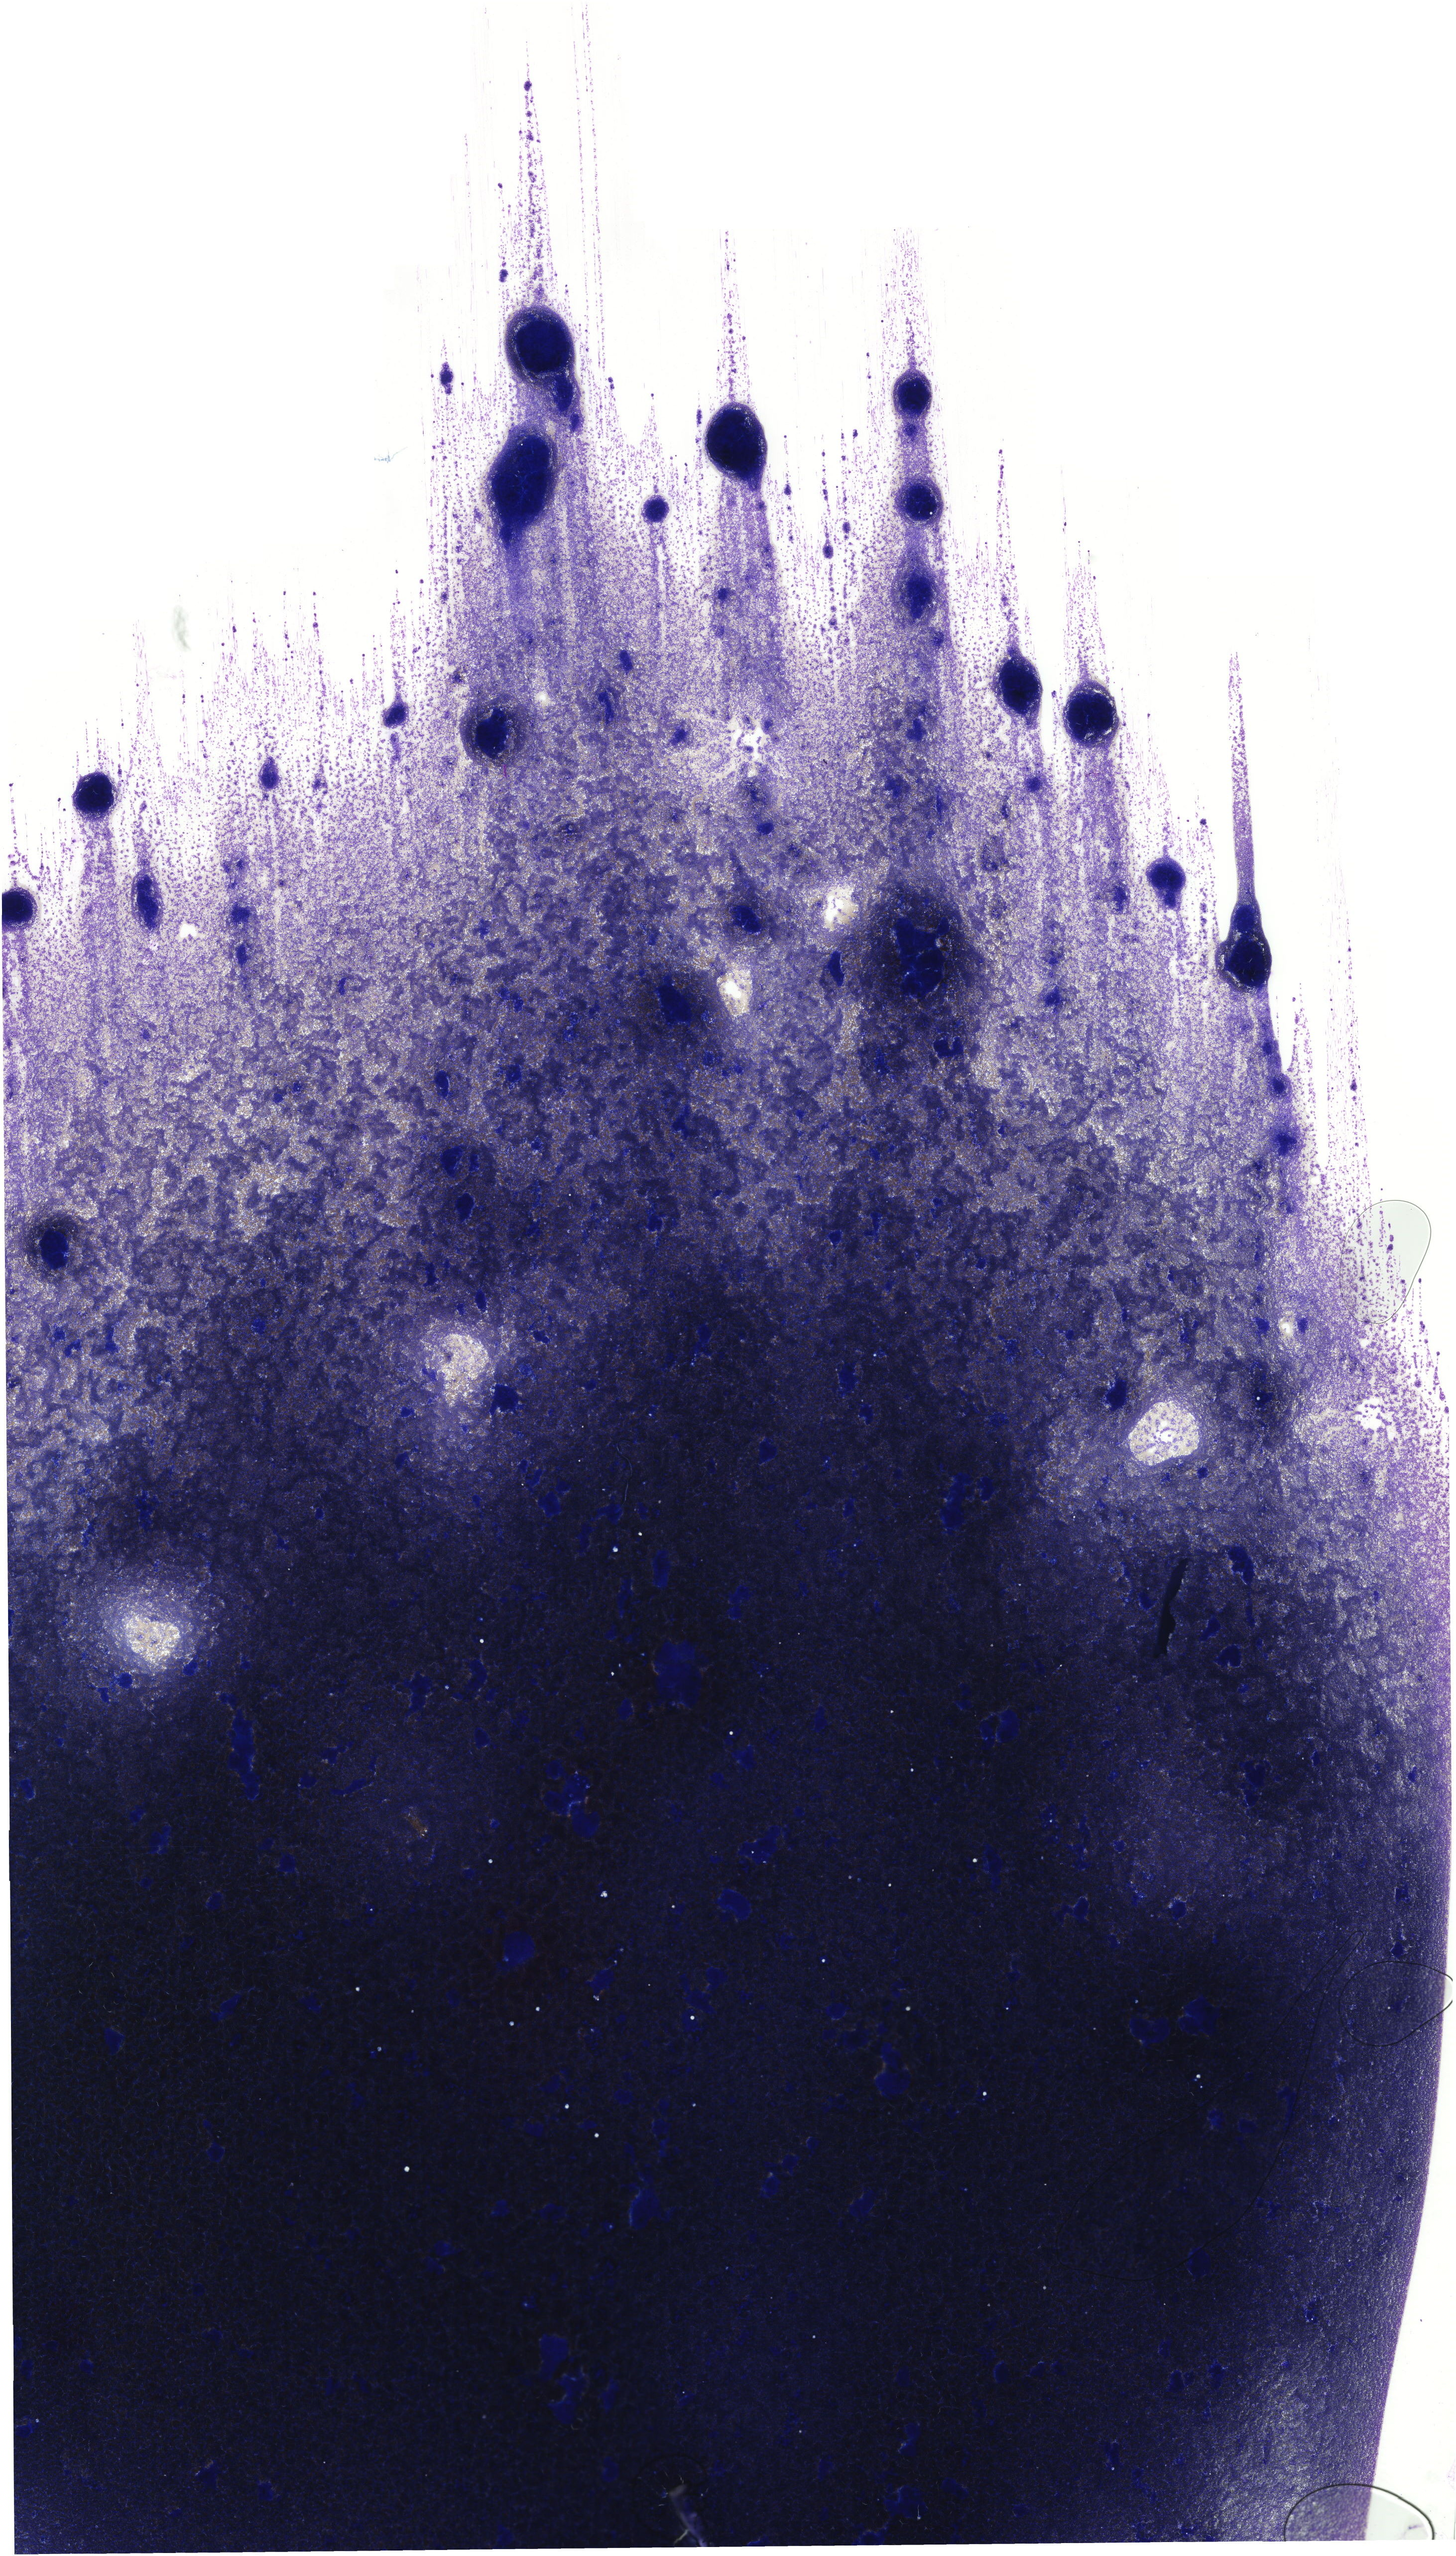
Whole-slide image of a May-Grünwald-Giemsa (MGG)-stained bone marrow aspirate smear — shown as a low-resolution overview of the whole scanned area (about 20.7 x 36.4 mm). Male patient.
- diagnosis: Chronic Phase Chronic Myeloid Leukemia, BCR-ABL1 Positive